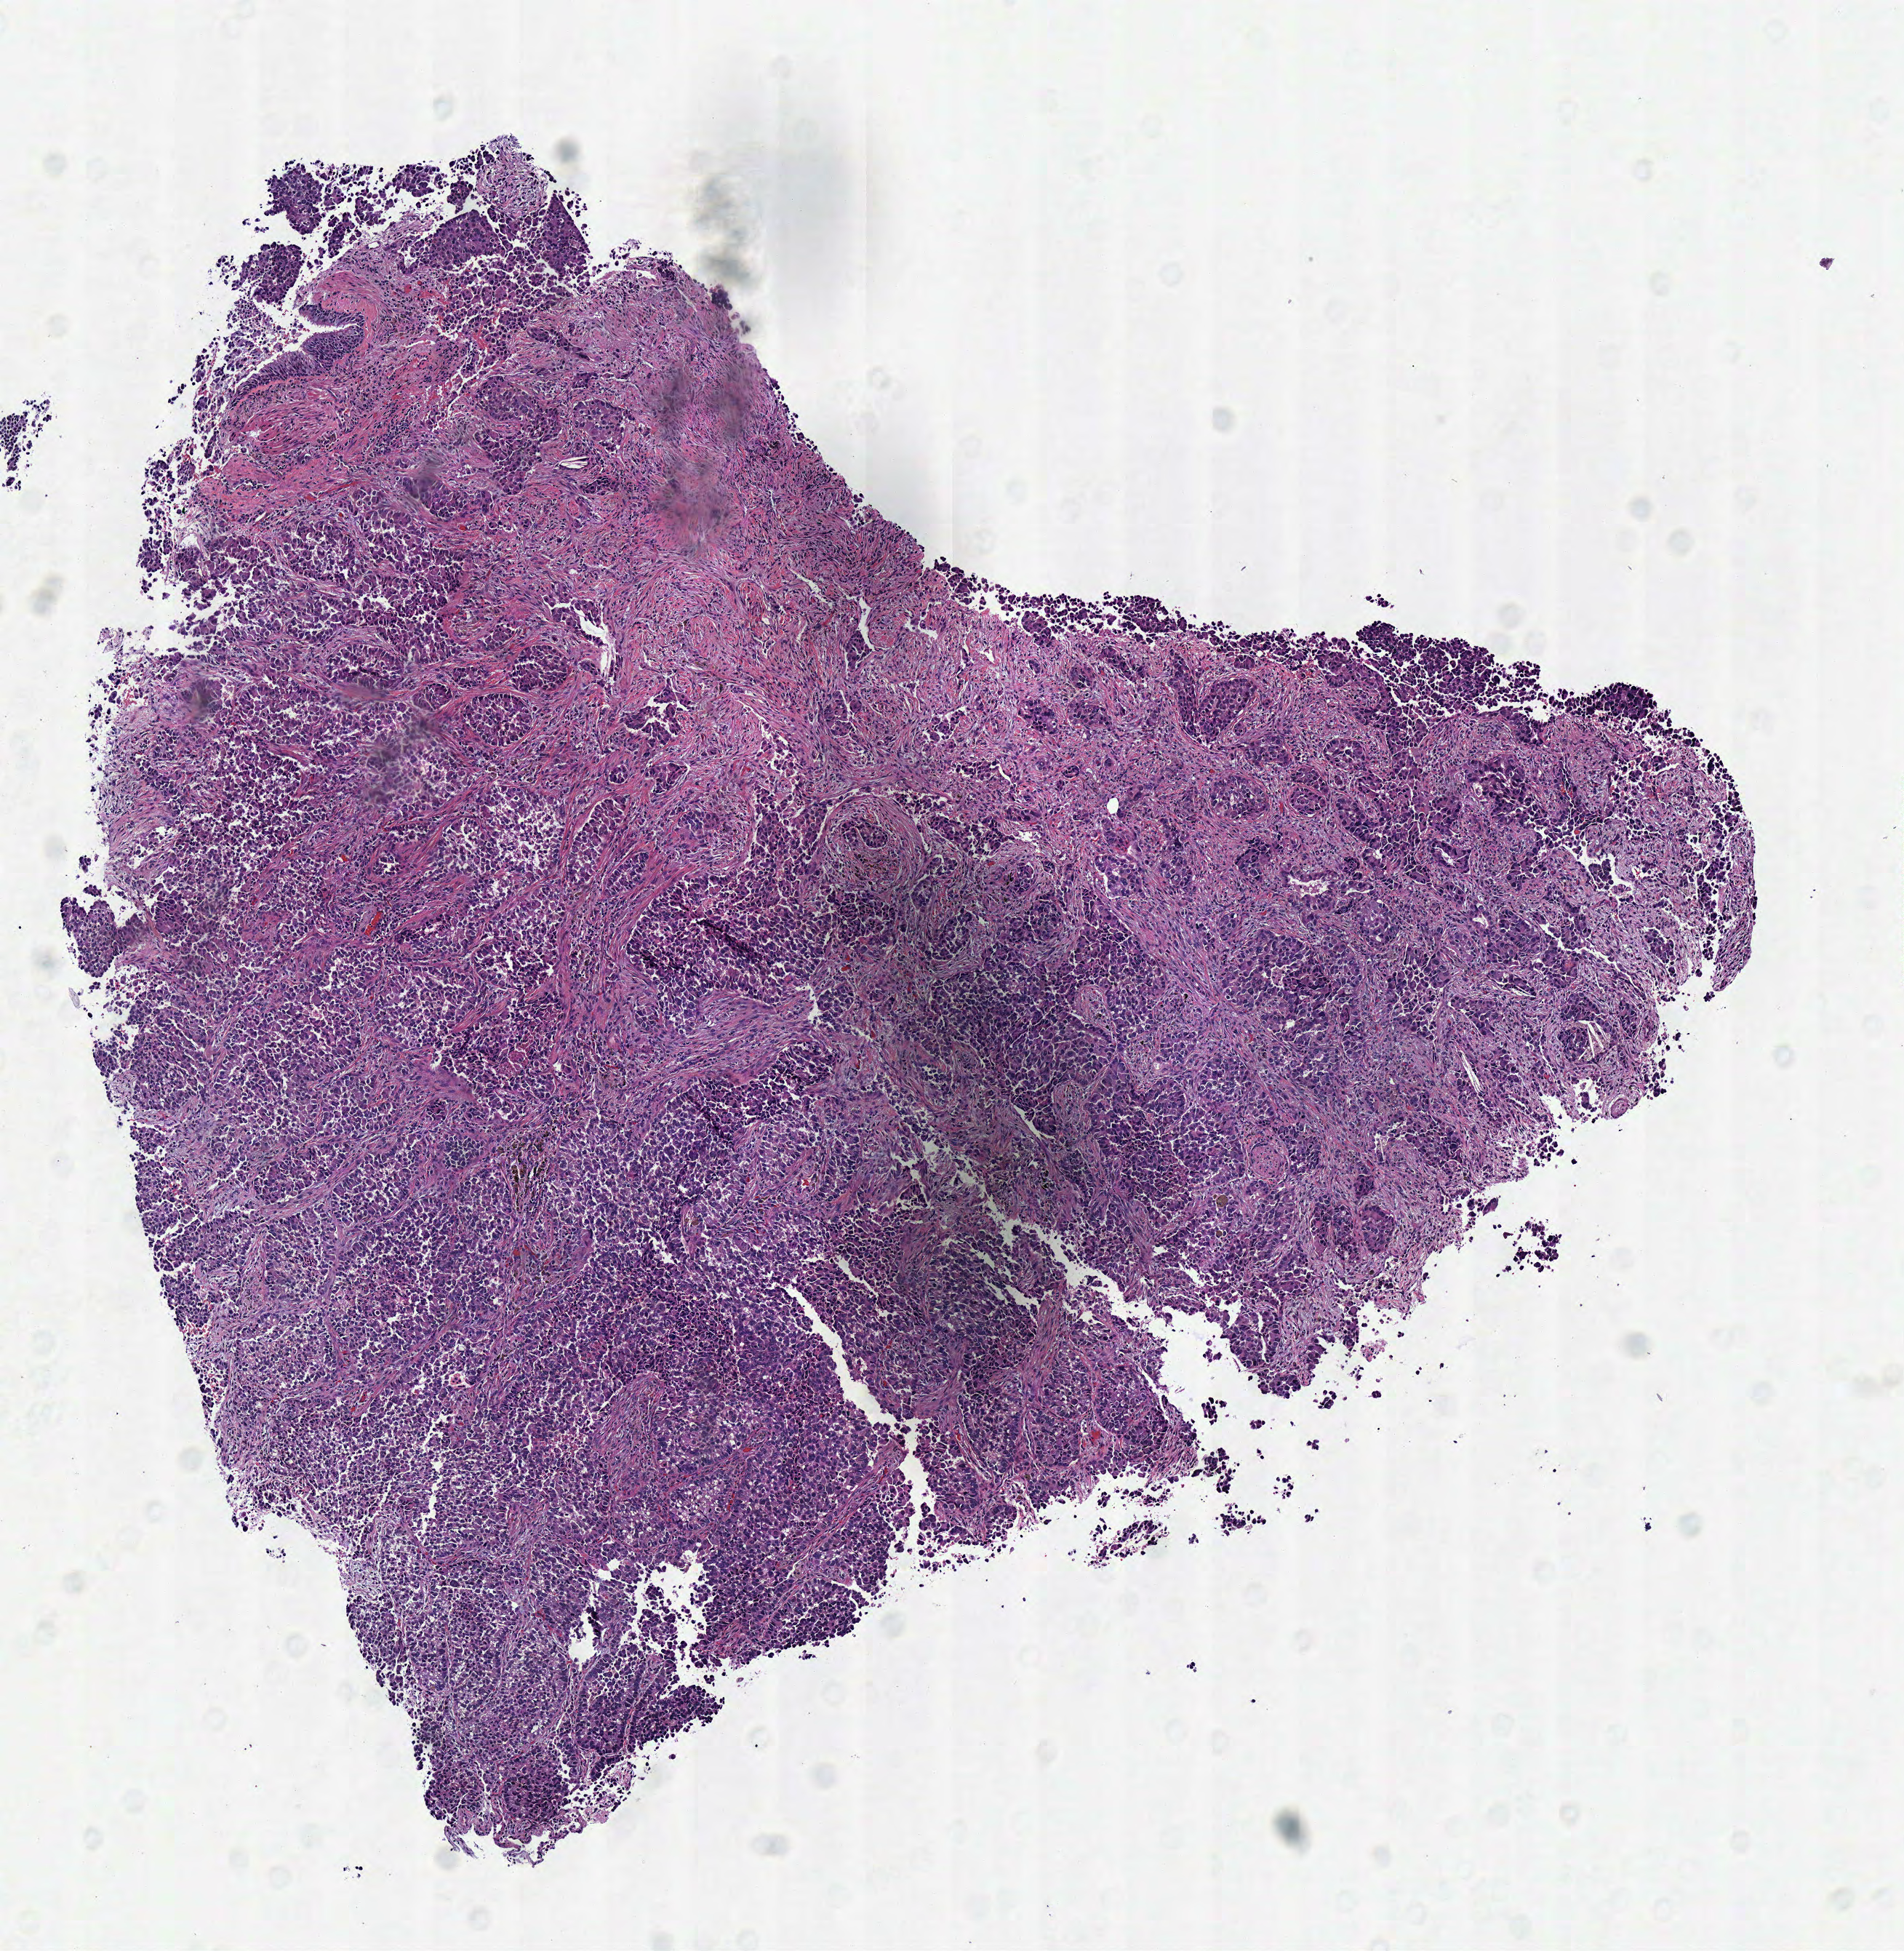
Whole-slide histology image, H&E, shown as a low-resolution overview of the whole scanned area (about 5.2 x 5.3 mm); frozen section from the top of the tissue portion; primary tumour sample from the lung. Male, age 58 years at initial diagnosis. Slide review estimates, as recorded: tumour cells 98%, tumour nuclei 80%, normal cells 1%, stromal cells 0%, necrosis 1%. Inflammatory infiltration, as recorded: lymphocyte infiltration 10%, monocyte infiltration 1%, neutrophil infiltration 2%.
Diagnosis: Adenocarcinoma, NOS (upper lobe, lung). AJCC pathologic stage: IA (7th edition).